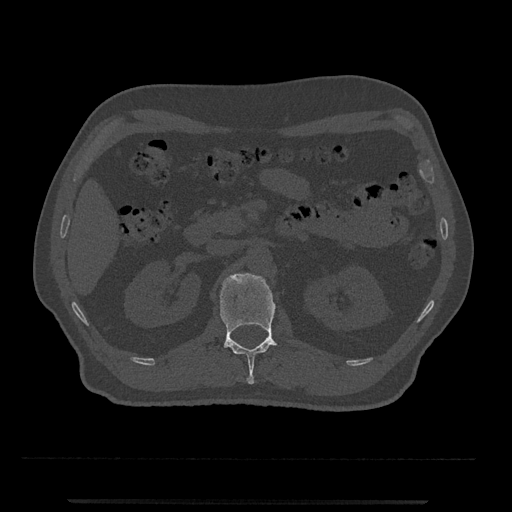
CT including the spine, one axial slice; bone window (W 1800 / L 400 HU); 0.5 mm slice thickness; 512 × 512 image matrix, field of view 419 × 419 mm. Male patient, age 63 years. From the clinical record (not read from this slice): primary cancer: prostate.
Annotated regions visible in this slice (semi-automatically segmented with operator editing):
- L1 vertebra: bounding box (x1, y1, x2, y2) in pixels: (220, 273, 279, 384)